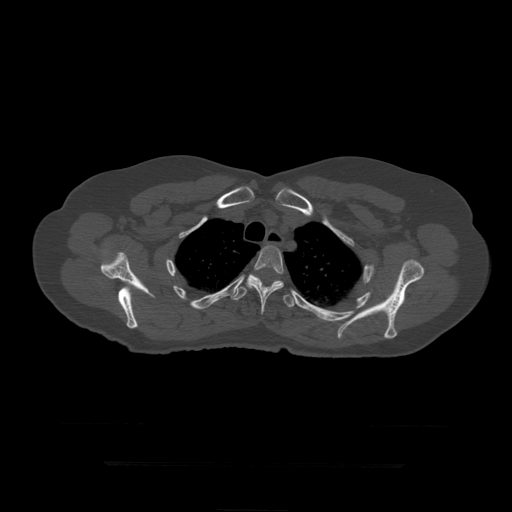
CT including the spine, one axial slice; position 346 of 399 along the scan axis; reconstruction kernel STANDARD; 120 kVp; bone window (W 1800 / L 400 HU); 1.25 mm slice thickness; 512 × 512 image matrix, field of view 450 × 450 mm. Patient age 41 years. From the clinical record (not read from this slice): primary cancer: breast.
Outlined on this slice (semi-automatically segmented with operator editing):
- T4 vertebra: box from (x=246, y=245) to (x=284, y=315) px
- T5 vertebra: (x=231, y=274)–(x=296, y=308)